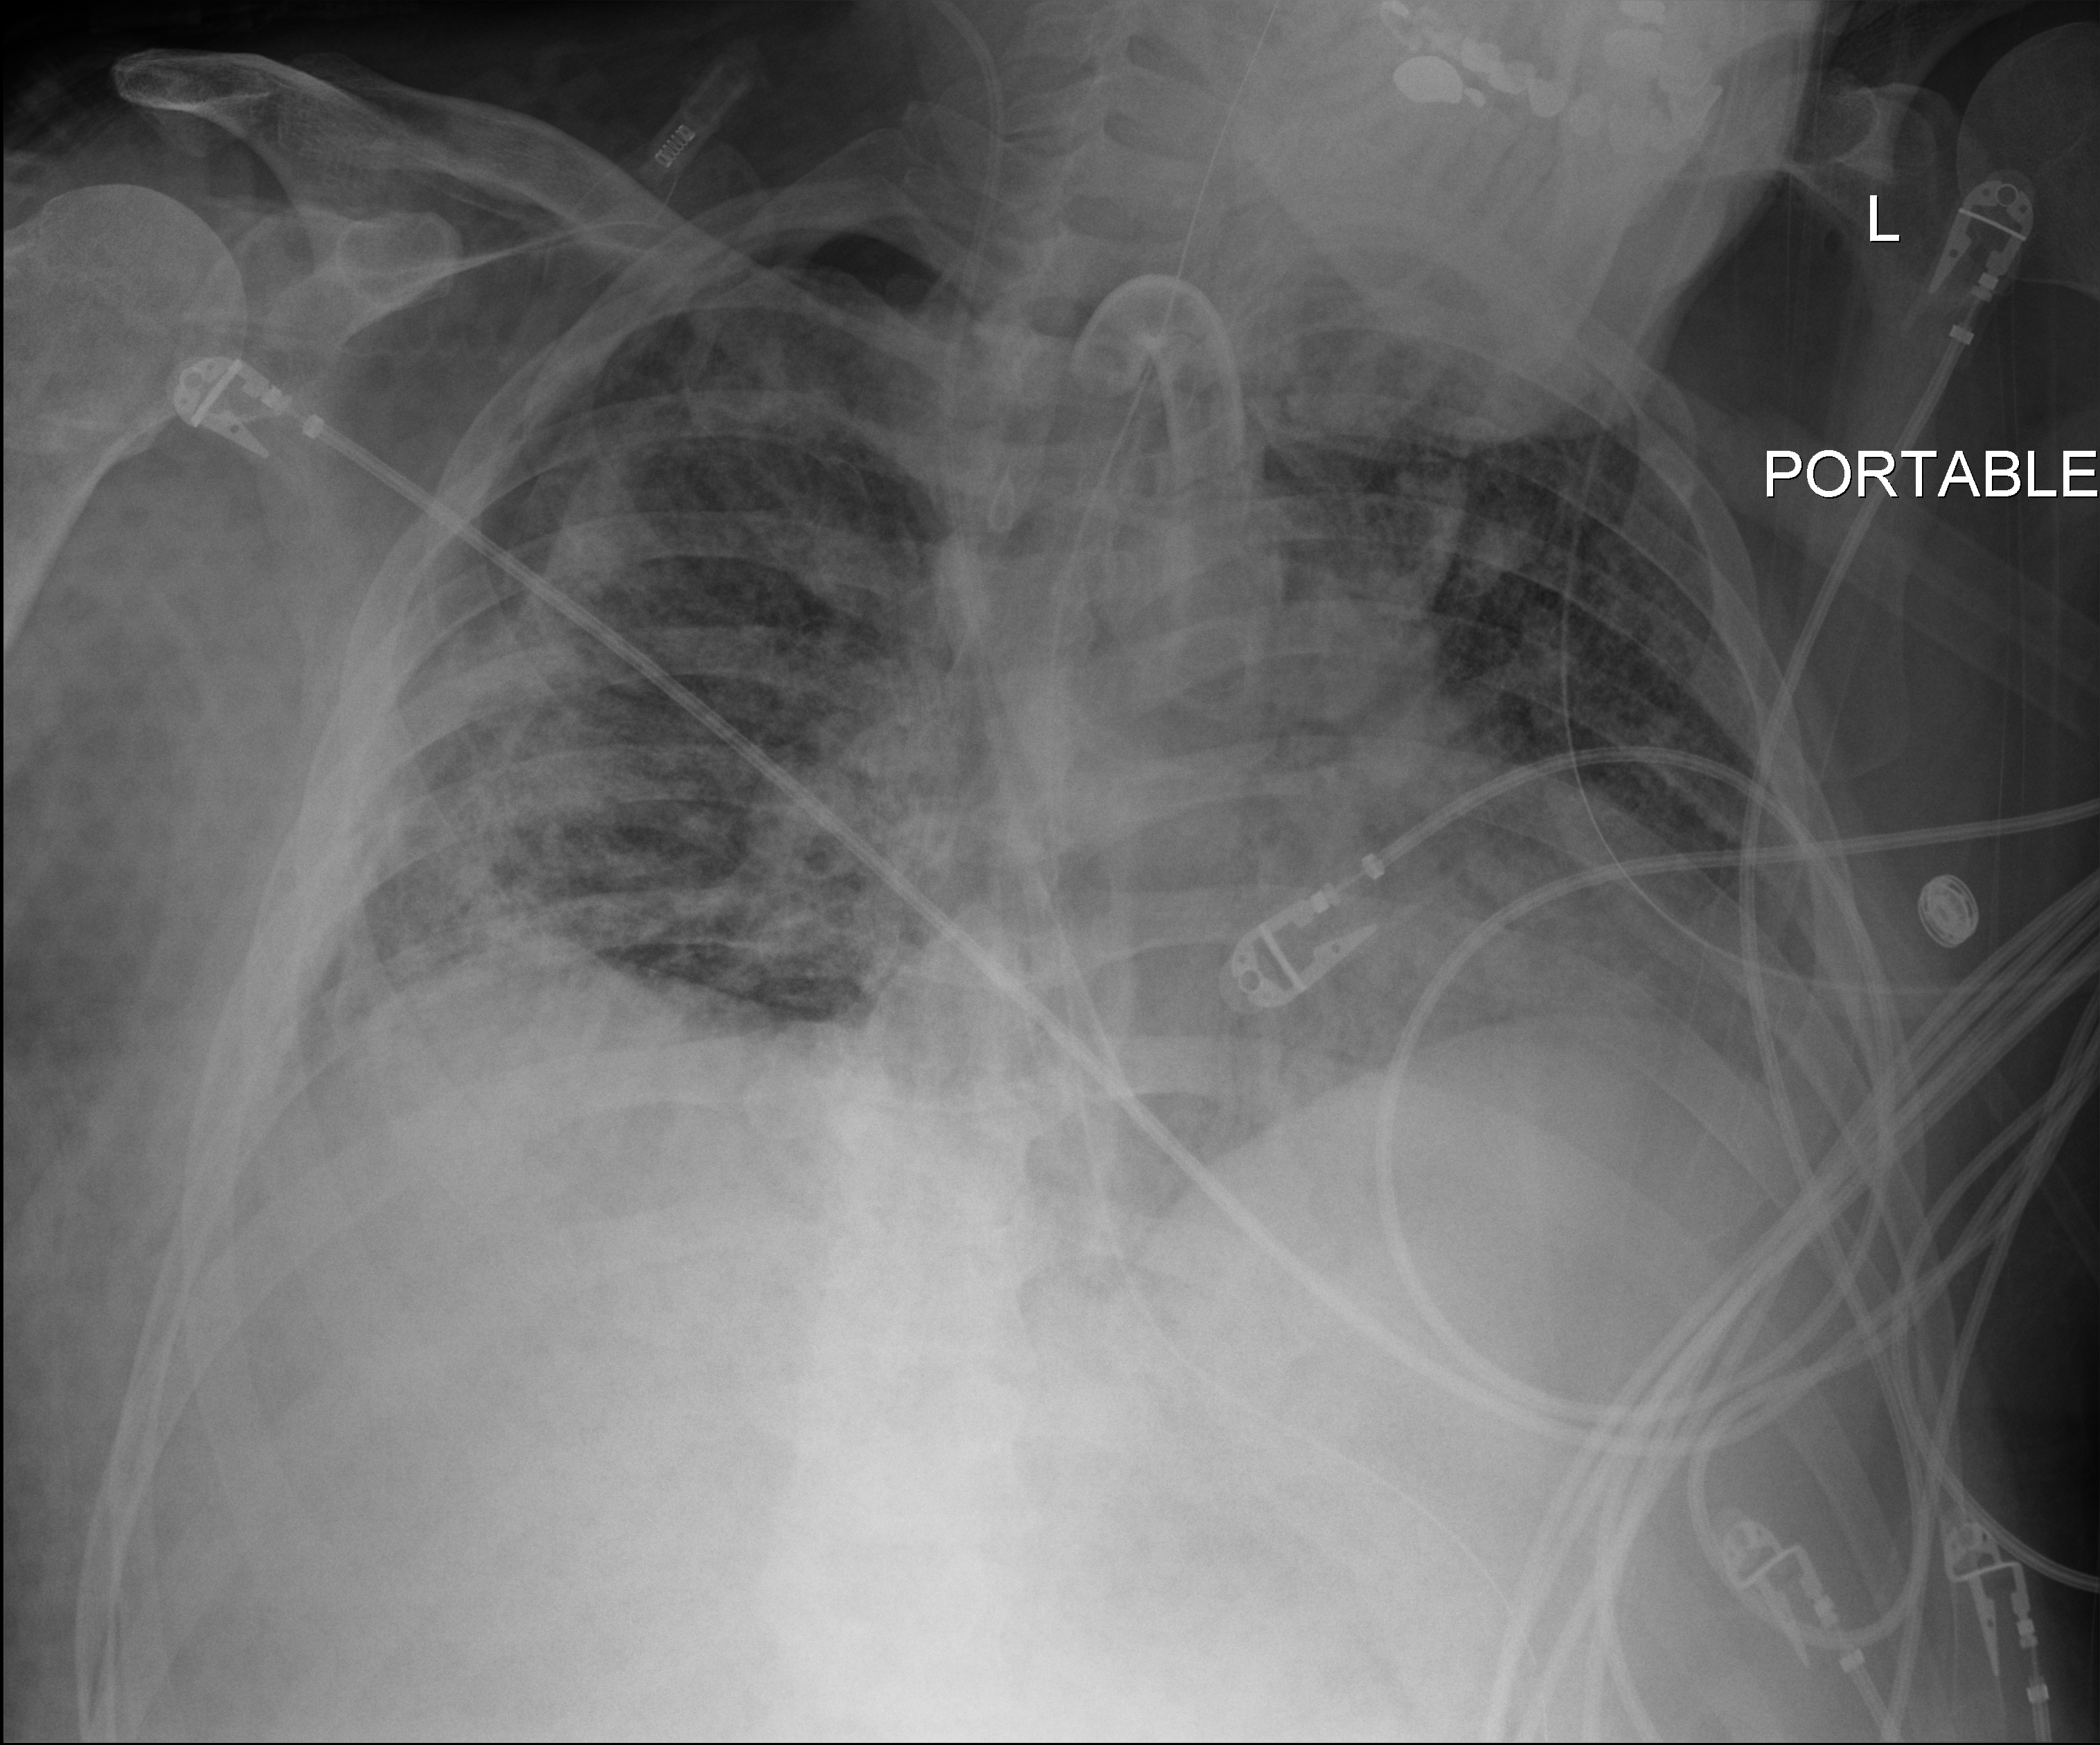
Chest X-ray (portable); anteroposterior (AP) projection. Male patient hospitalised with COVID-19, age 18–59 years.
From the hospital-stay record, not from the radiograph (when in the stay this image was taken is not recorded):
- admitted to intensive care during this hospital stay: yes
- mechanically ventilated during this hospital stay: yes